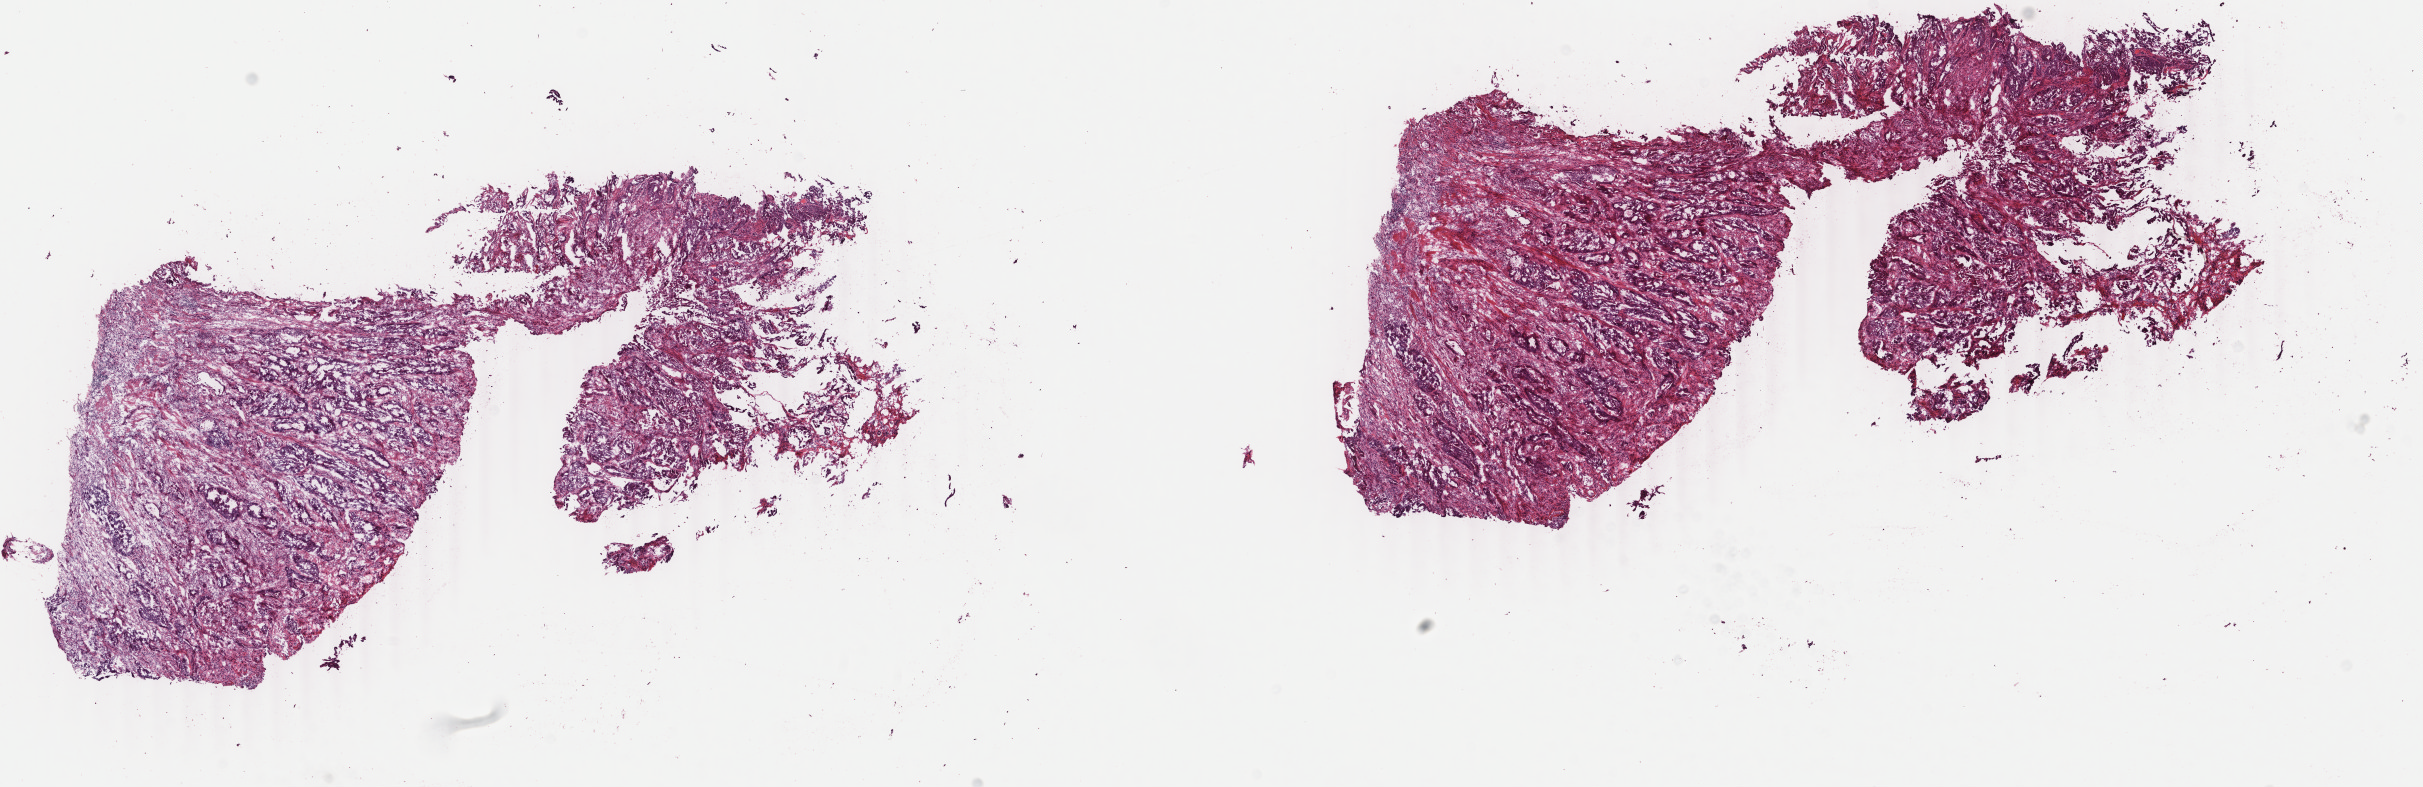
Hematoxylin and eosin (H&E) stained whole-slide image — a low-resolution overview of the entire scanned area, about 19.3 x 6.3 mm (acquisition: 40x scan); frozen section from the bottom of the tissue portion; colon, primary tumour sample. Male patient; age at initial diagnosis 65 years. Composition of this section per pathologist review: tumour cells 65%, tumour nuclei 70%, normal cells 0%, stromal cells 25%, necrosis 10%. Inflammatory infiltration, as recorded: lymphocyte infiltration 3%, monocyte infiltration 0%, neutrophil infiltration 0%.
TNM: T3 N0 M0. Diagnosis: Adenocarcinoma, NOS (cecum). AJCC pathologic stage: IIA.